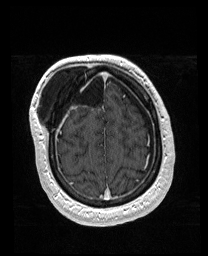
Brain MRI from a brain-tumour surgery series, one axial slice; slice 44 of 176 in the series (ordered by position); T1-weighted post-contrast; 1 mm slice thickness; 208 × 256 image matrix, field of view 208 × 256 mm. From the clinical record (not read from this slice): histopathology: Astrocytoma; WHO grade: 4; IDH mutation: yes; tumour location: Right Orbitofrontal Anterior Temporal Insular.
Annotated regions visible in this slice (expert manual segmentation):
- previous resection cavity: box from (x=73, y=71) to (x=103, y=107) px